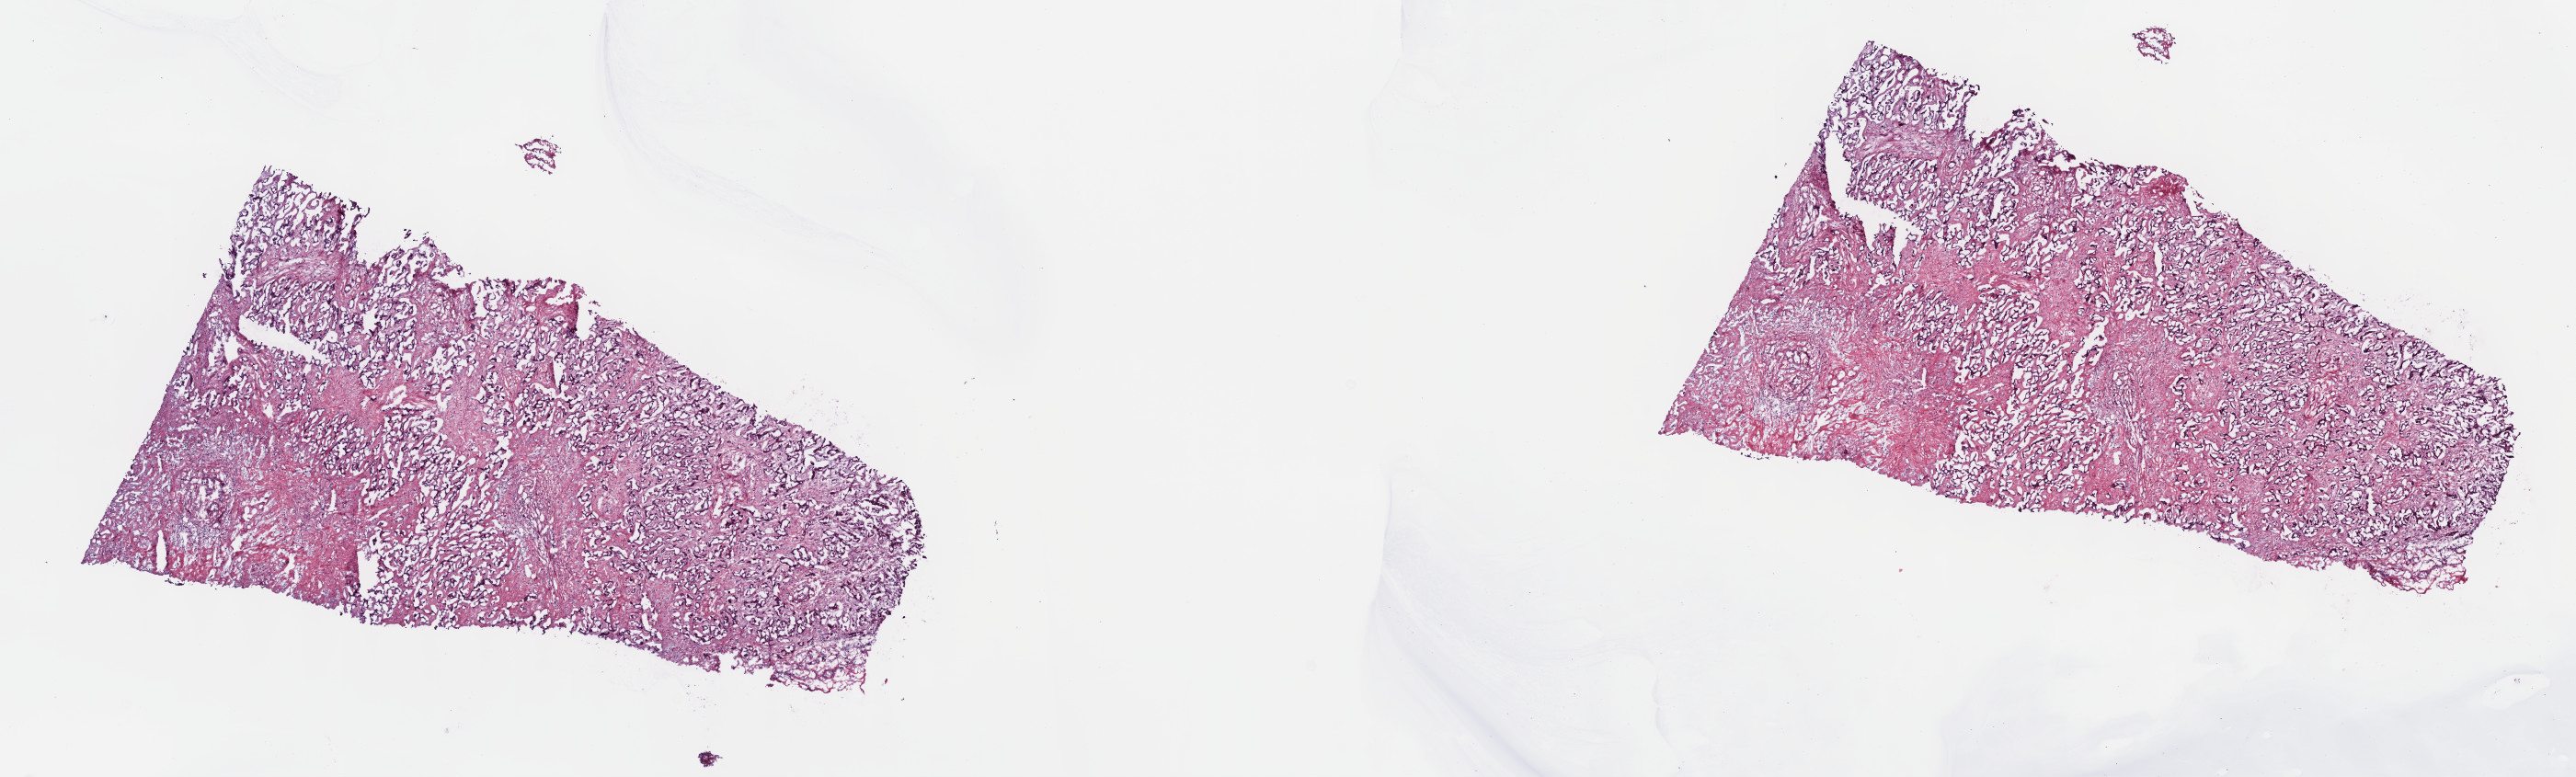
Digitized Hematoxylin and eosin (H&E) stained tissue section (whole slide) — whole scanned area (about 22.7 x 6.8 mm) shown as a low-resolution overview, frozen section from the top of the tissue portion, bile duct, primary tumour sample. Patient: male, age at initial diagnosis 52 years.
Histologic diagnosis: Cholangiocarcinoma.